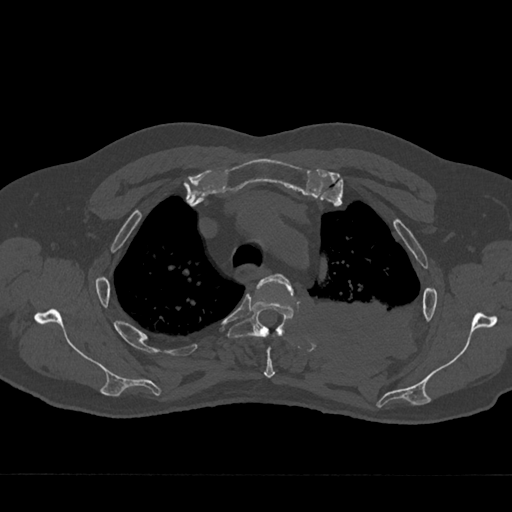
CT including the spine, one axial slice; slice 537 of 797 in the series (ordered by position); reconstruction kernel Br40s/3; 120 kVp; bone window (W 1800 / L 400 HU); 0.5 mm slice thickness; 512 × 512 image matrix, field of view 377 × 377 mm. Male patient, age 75 years. From the clinical record (not read from this slice): primary cancer: renal.
Structures marked on this image (semi-automatically segmented with operator editing):
- T3 vertebra: box from (x=257, y=274) to (x=294, y=378) px
- T4 vertebra: (x=227, y=297)–(x=294, y=338)